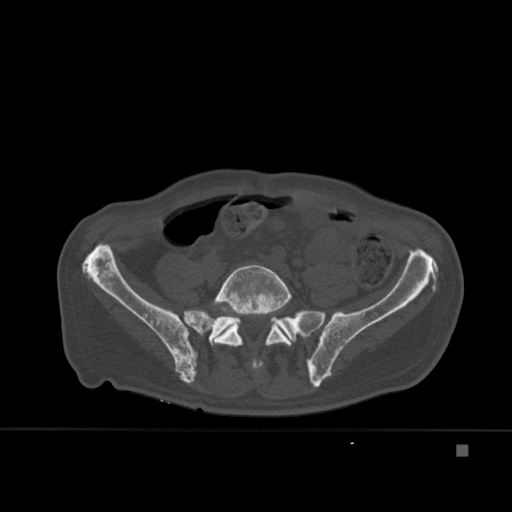
CT including the spine, one axial slice. Slice 98 of 451 in the series (ordered by position). Bone window (W 1800 / L 400 HU). 1.5 mm slice thickness. 512 × 512 image matrix, field of view 378 × 378 mm. Male patient, age 75 years. From the clinical record (not read from this slice): primary cancer: prostate.
Annotated regions visible in this slice (semi-automatically segmented with operator editing):
- L5 vertebra: bounding box [x1, y1, x2, y2] px = [212, 264, 292, 369]
- T7 vertebra: [216, 300, 241, 330]